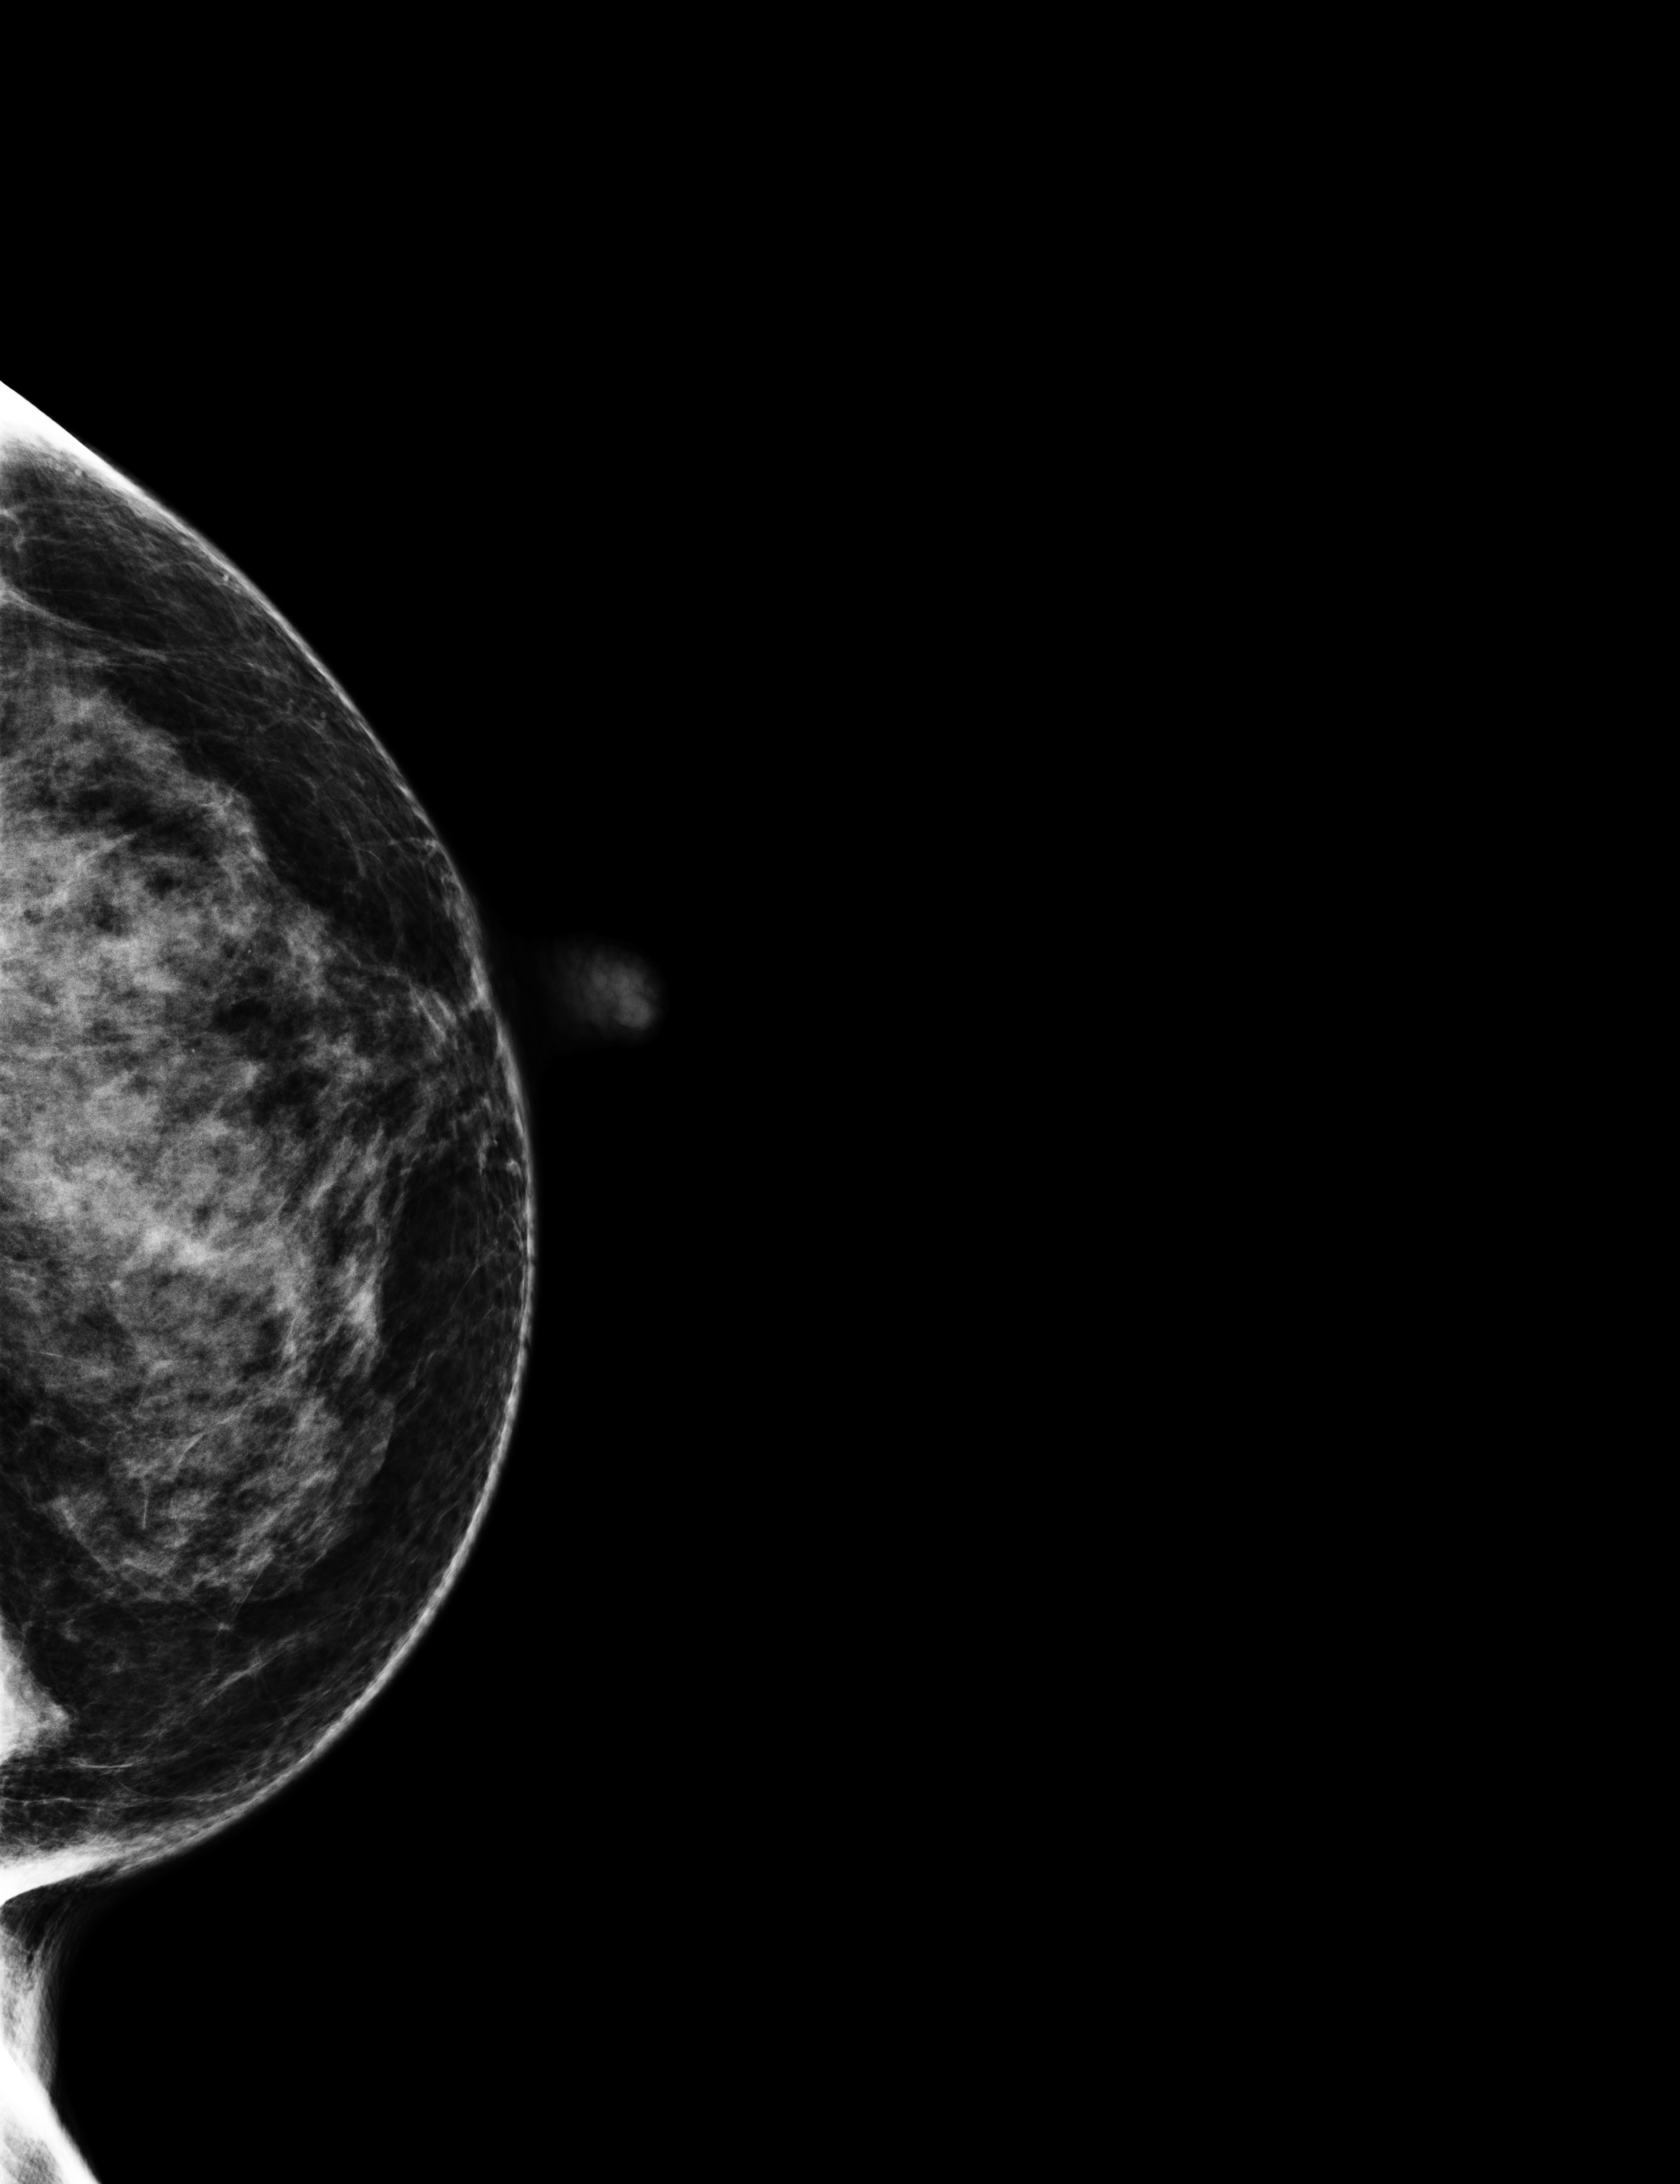
Digital mammogram (FFDM), left breast, cranio-caudal projection, annual screening mammography examination. Patient aged 53 years (female).
- breast density at the screening exam (both breasts): extremely dense (BI-RADS density category d)
- final BI-RADS category for the screening round (tomosynthesis exam, both breasts): category 2
- recall: no recall after this screen